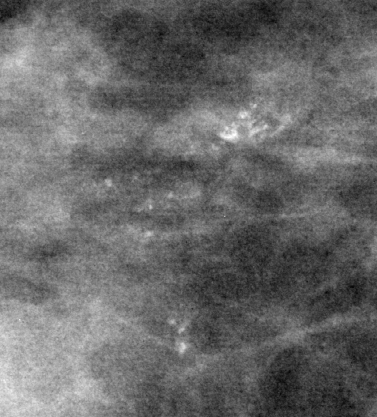
Cropped region of a digitized screen-film mammogram centred on a radiologist-marked abnormality, right breast, CC view.
Marked abnormality: calcifications, morphology pleomorphic / fine linear branching, distribution clustered; BI-RADS assessment category 4; subtlety rating 3 on a 1 (subtle) to 5 (obvious) scale; pathology (as recorded): benign.